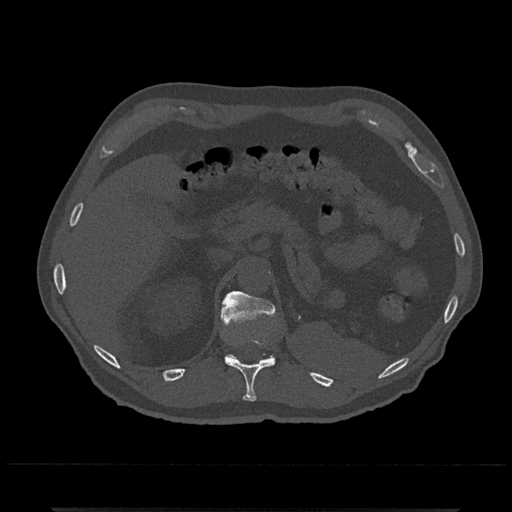
CT including the spine, one axial slice; slice 468 of 797 in the series (ordered by position); reconstruction kernel Br40s/3; bone window (W 1800 / L 400 HU); 512 × 512 image matrix. Male patient, age 67 years. From the clinical record (not read from this slice): primary cancer: prostate.
Annotated regions visible in this slice (semi-automatically segmented with operator editing):
- T11 vertebra: box from (x=225, y=336) to (x=276, y=402) px
- T12 vertebra: (x=221, y=291)–(x=278, y=360)